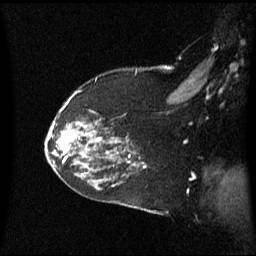
Breast MRI (dynamic contrast-enhanced), one sagittal slice. Position 46 of 60 along the scan axis. Dynamic contrast-enhanced series, image 2 of 3 at this slice position (ordered by acquisition). 1.5 T. TE 4.2 ms, TR 8.4 ms. 2 mm slice thickness. 256 × 256 image matrix, field of view 240 × 240 mm. Patient: female, 59 years. Case-level facts recorded for this patient, not image findings: setting: breast cancer imaged before/during neoadjuvant chemotherapy; receptor status: HR-positive, HER2-negative.
Outlined on this slice (semi-automatically segmented with operator editing):
- analysis volume of interest (the breast-tissue region the enhancement analysis was run in; not a lesion): bounding box [x1, y1, x2, y2] px = [46, 122, 89, 163]
- tumour enhancement mask (voxels above the 70 % enhancement threshold inside the analysis volume of interest): [67, 134, 72, 141]